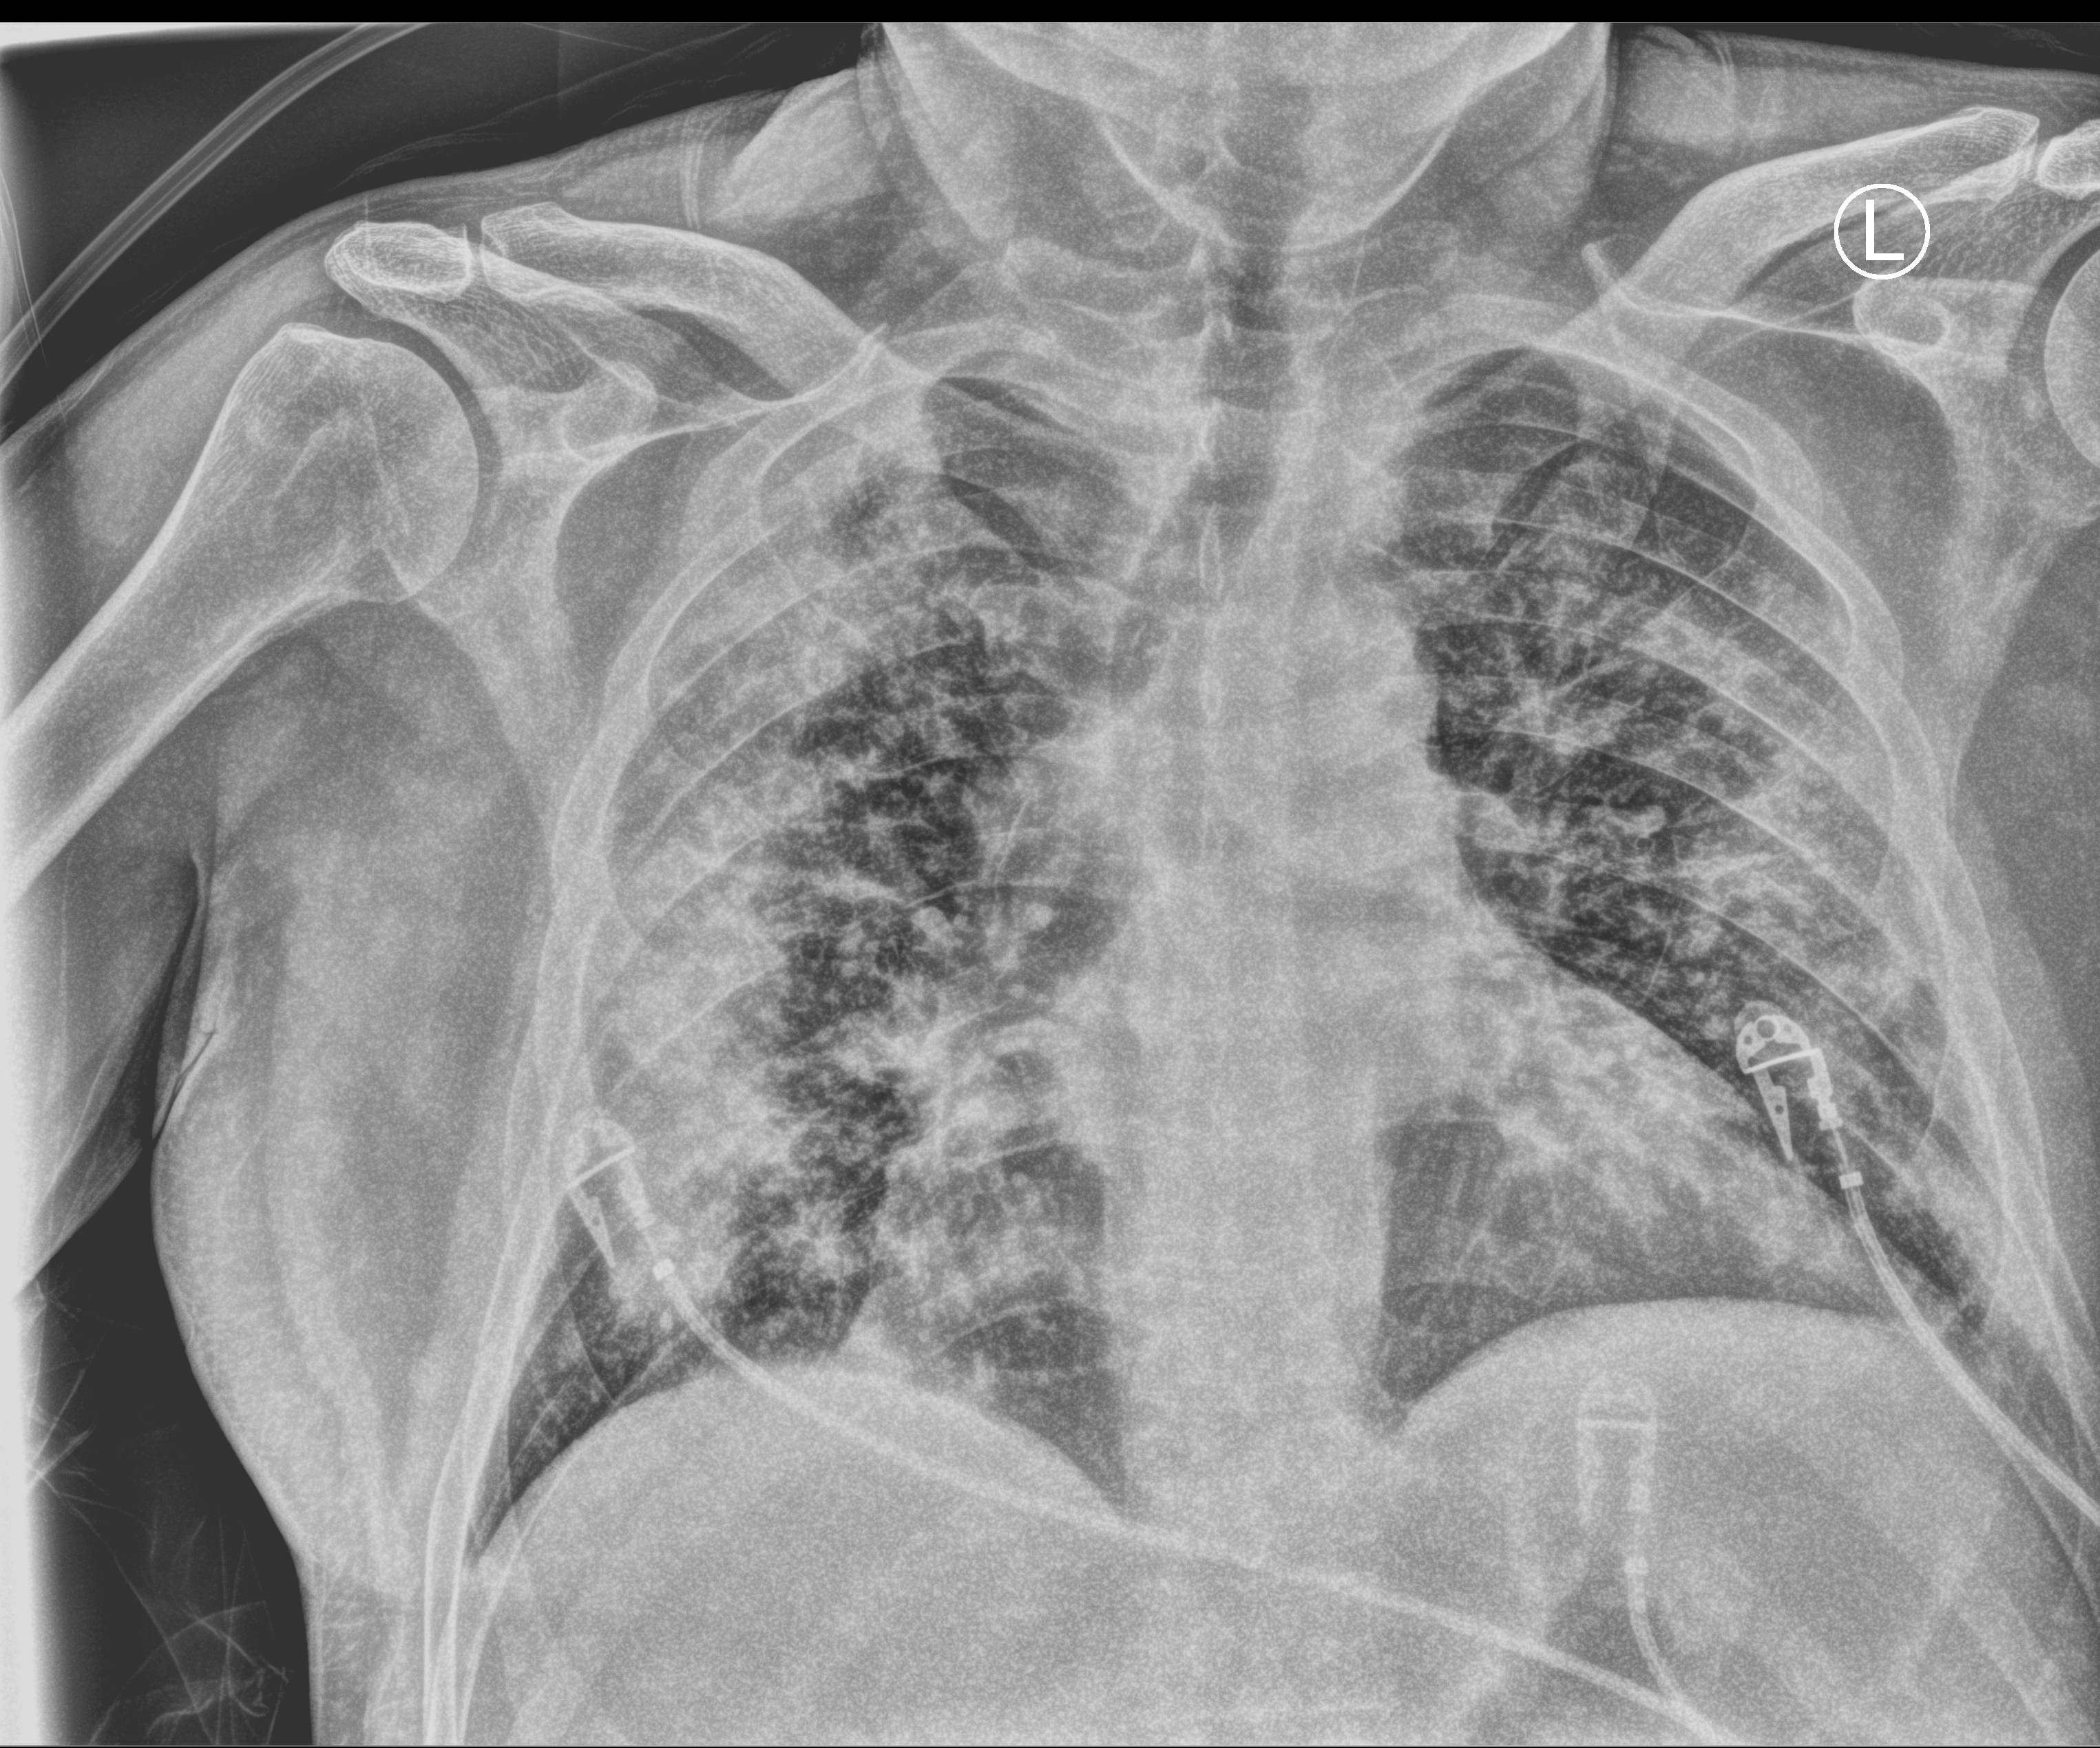
Chest X-ray (portable); anteroposterior (AP) projection. Patient hospitalised with COVID-19; male, aged 60–74 years.
Admission-level facts for this patient (not findings on this image; timing relative to this image not recorded): admitted to intensive care during this hospital stay: no; mechanically ventilated during this hospital stay: no.